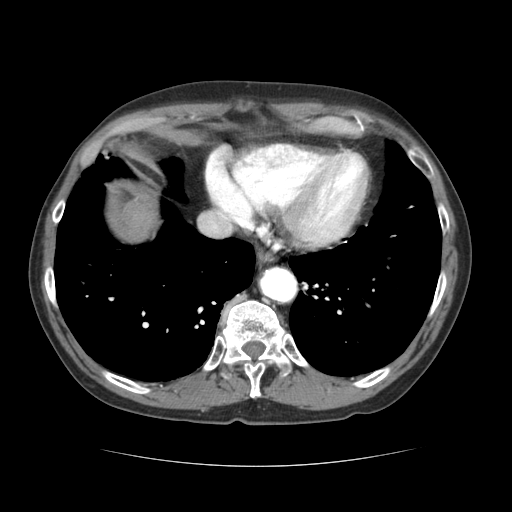
Contrast-enhanced abdominal CT (liver protocol), one axial slice; slice 61 of 69 in the series (ordered by position); 120 kVp; soft-tissue window (W 400 / L 40 HU); 2.5 mm slice thickness; 512 × 512 image matrix, field of view 360 × 360 mm. Case-level facts recorded for this patient, not image findings: diagnosis: hepatocellular carcinoma (patient treated with transarterial chemoembolisation; whether this scan precedes or follows treatment is not stated here); TNM stage (as recorded): Stage-II; Child-Pugh class: B; tumour differentiation: poorly differentiated; tumour nodularity: multinodular.
Structures marked on this image (semi-automatic segmentation, software-assisted and operator-edited):
- liver parenchyma outside the tumour (the mass and vessels are separate outlines, so this box may not span the whole liver): bounding box (x1, y1, x2, y2) in pixels: (112, 198, 156, 240)